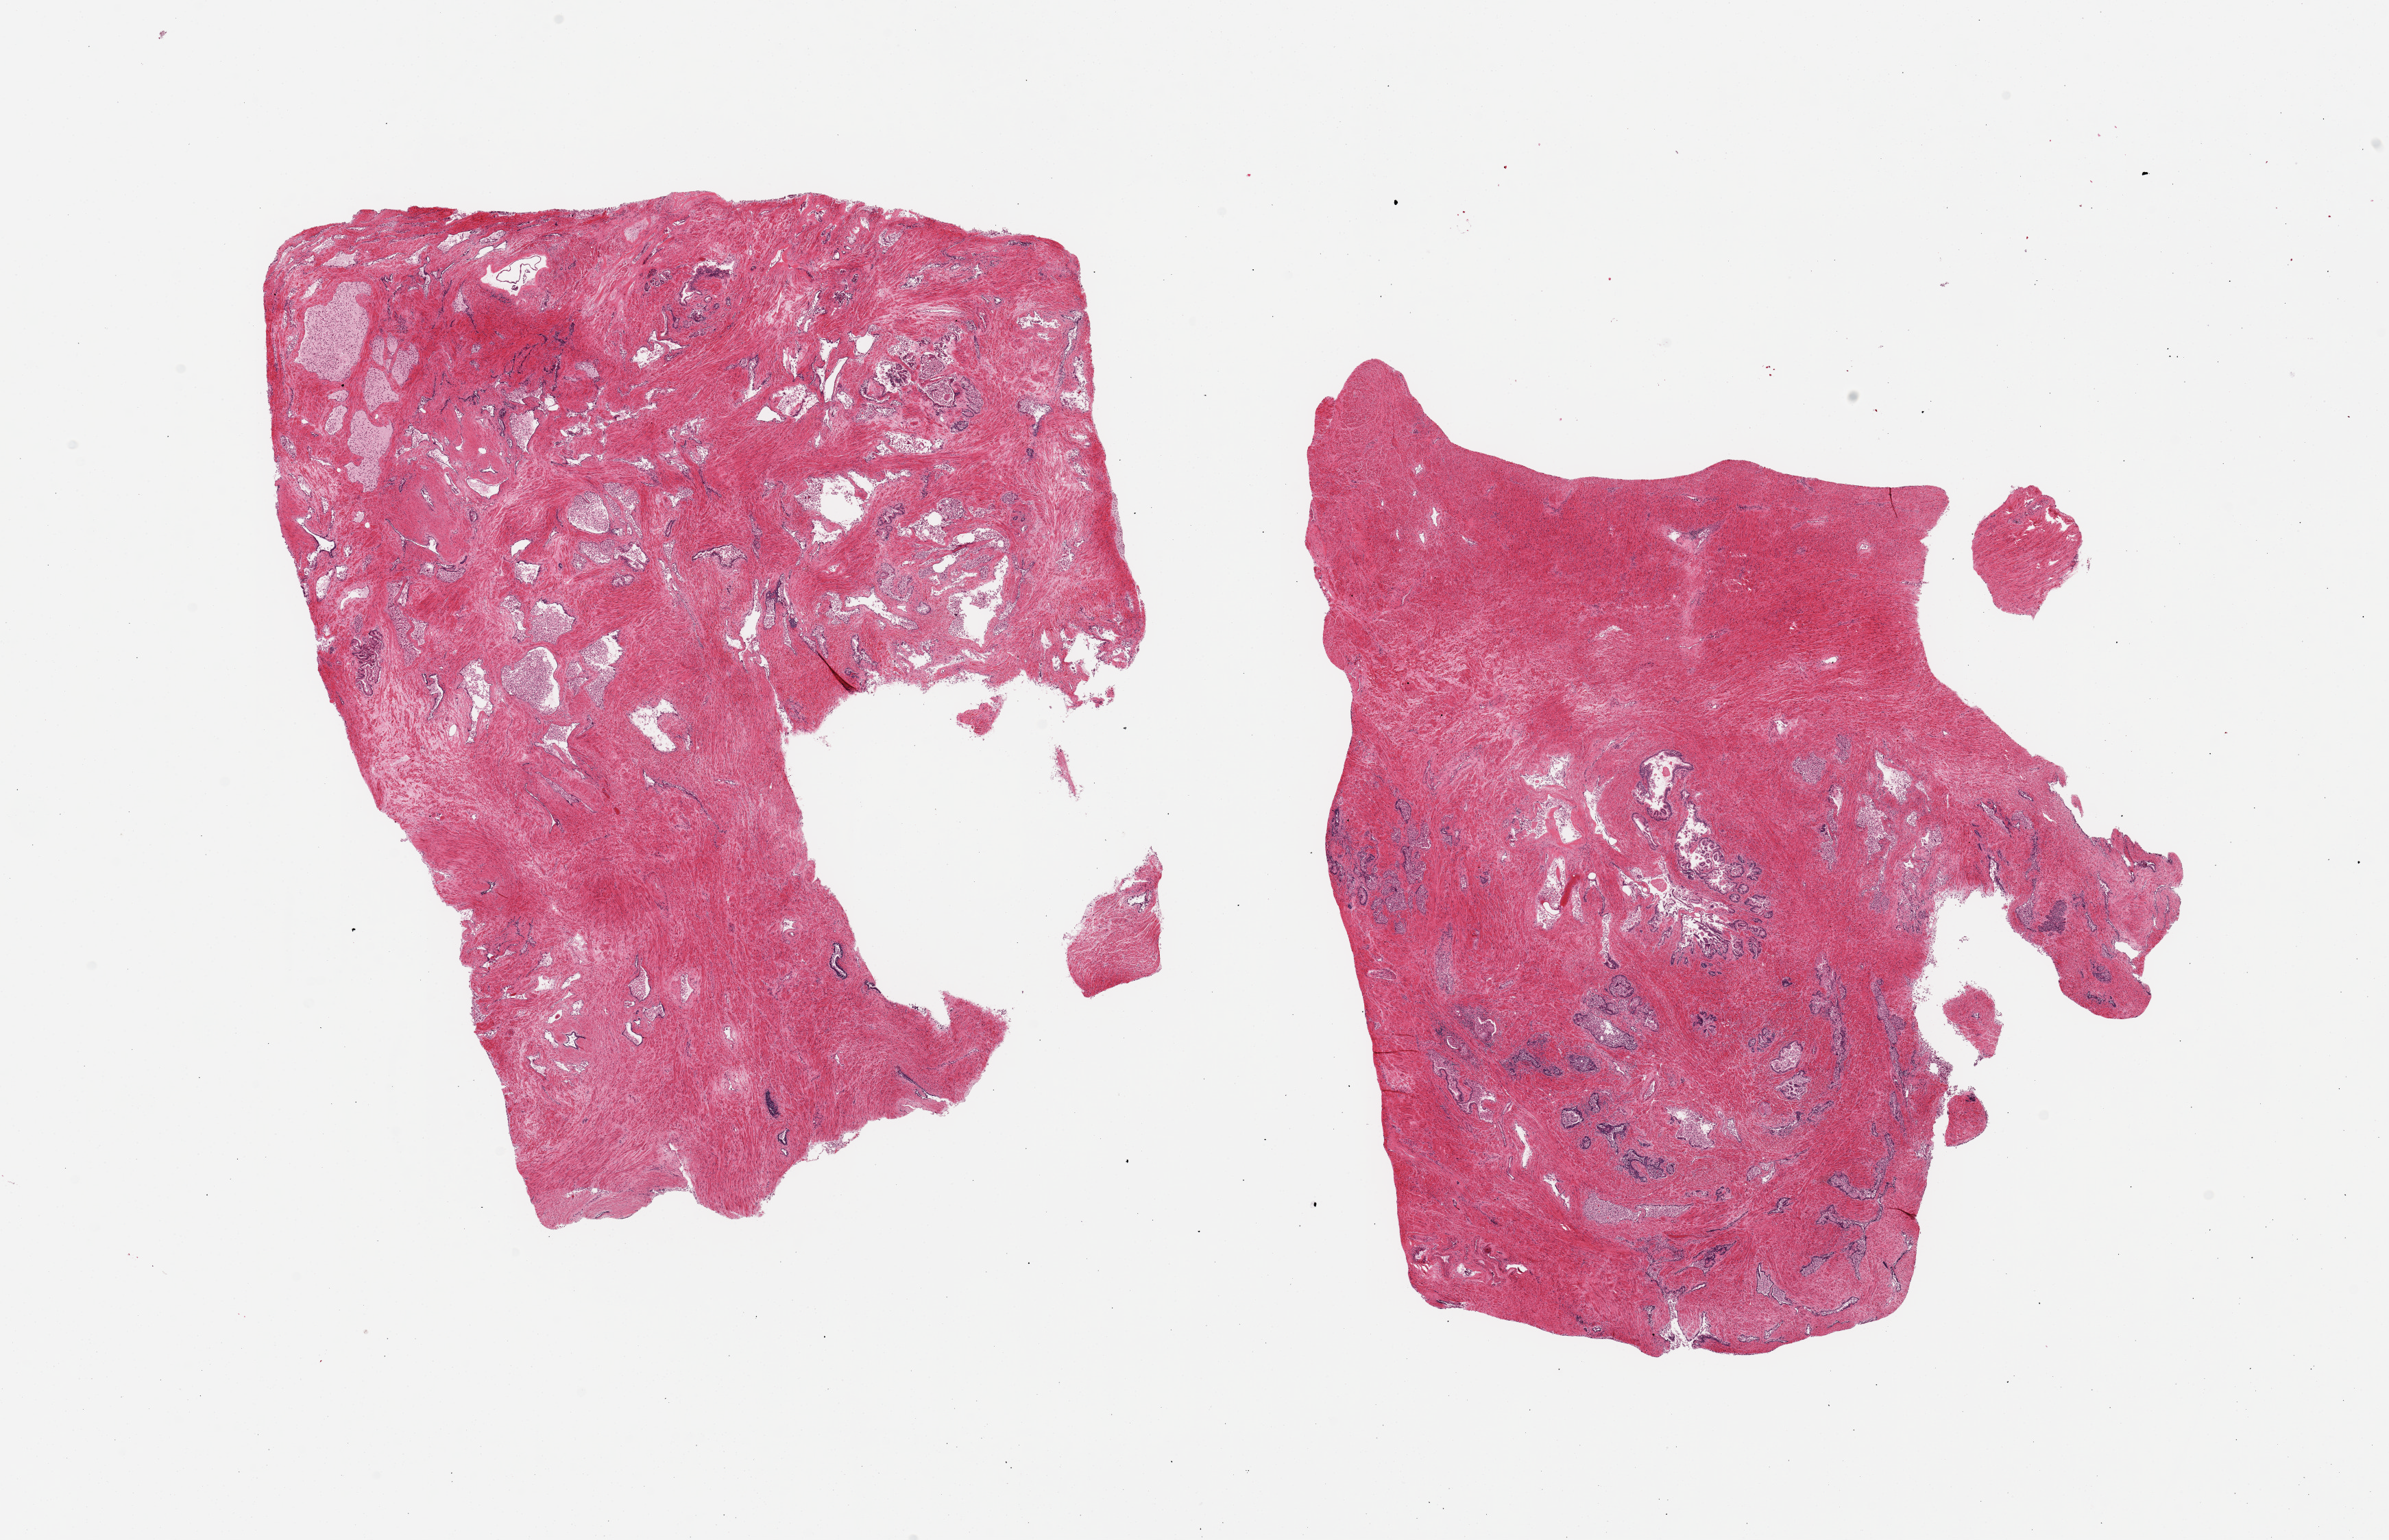
H&E whole-slide image, brightfield, low-resolution overview of the scanned area, about 27.6 x 17.8 mm (from a 20x scan). PAXgene-fixed, paraffin-embedded tissue. Section of prostate (target tissue). Donor tissue sample. Donor: male.
* reviewer comment on this tissue sample: 2 pieces; fibromuscular stroma predominates, glands largely autolyzed, focal prostatitis